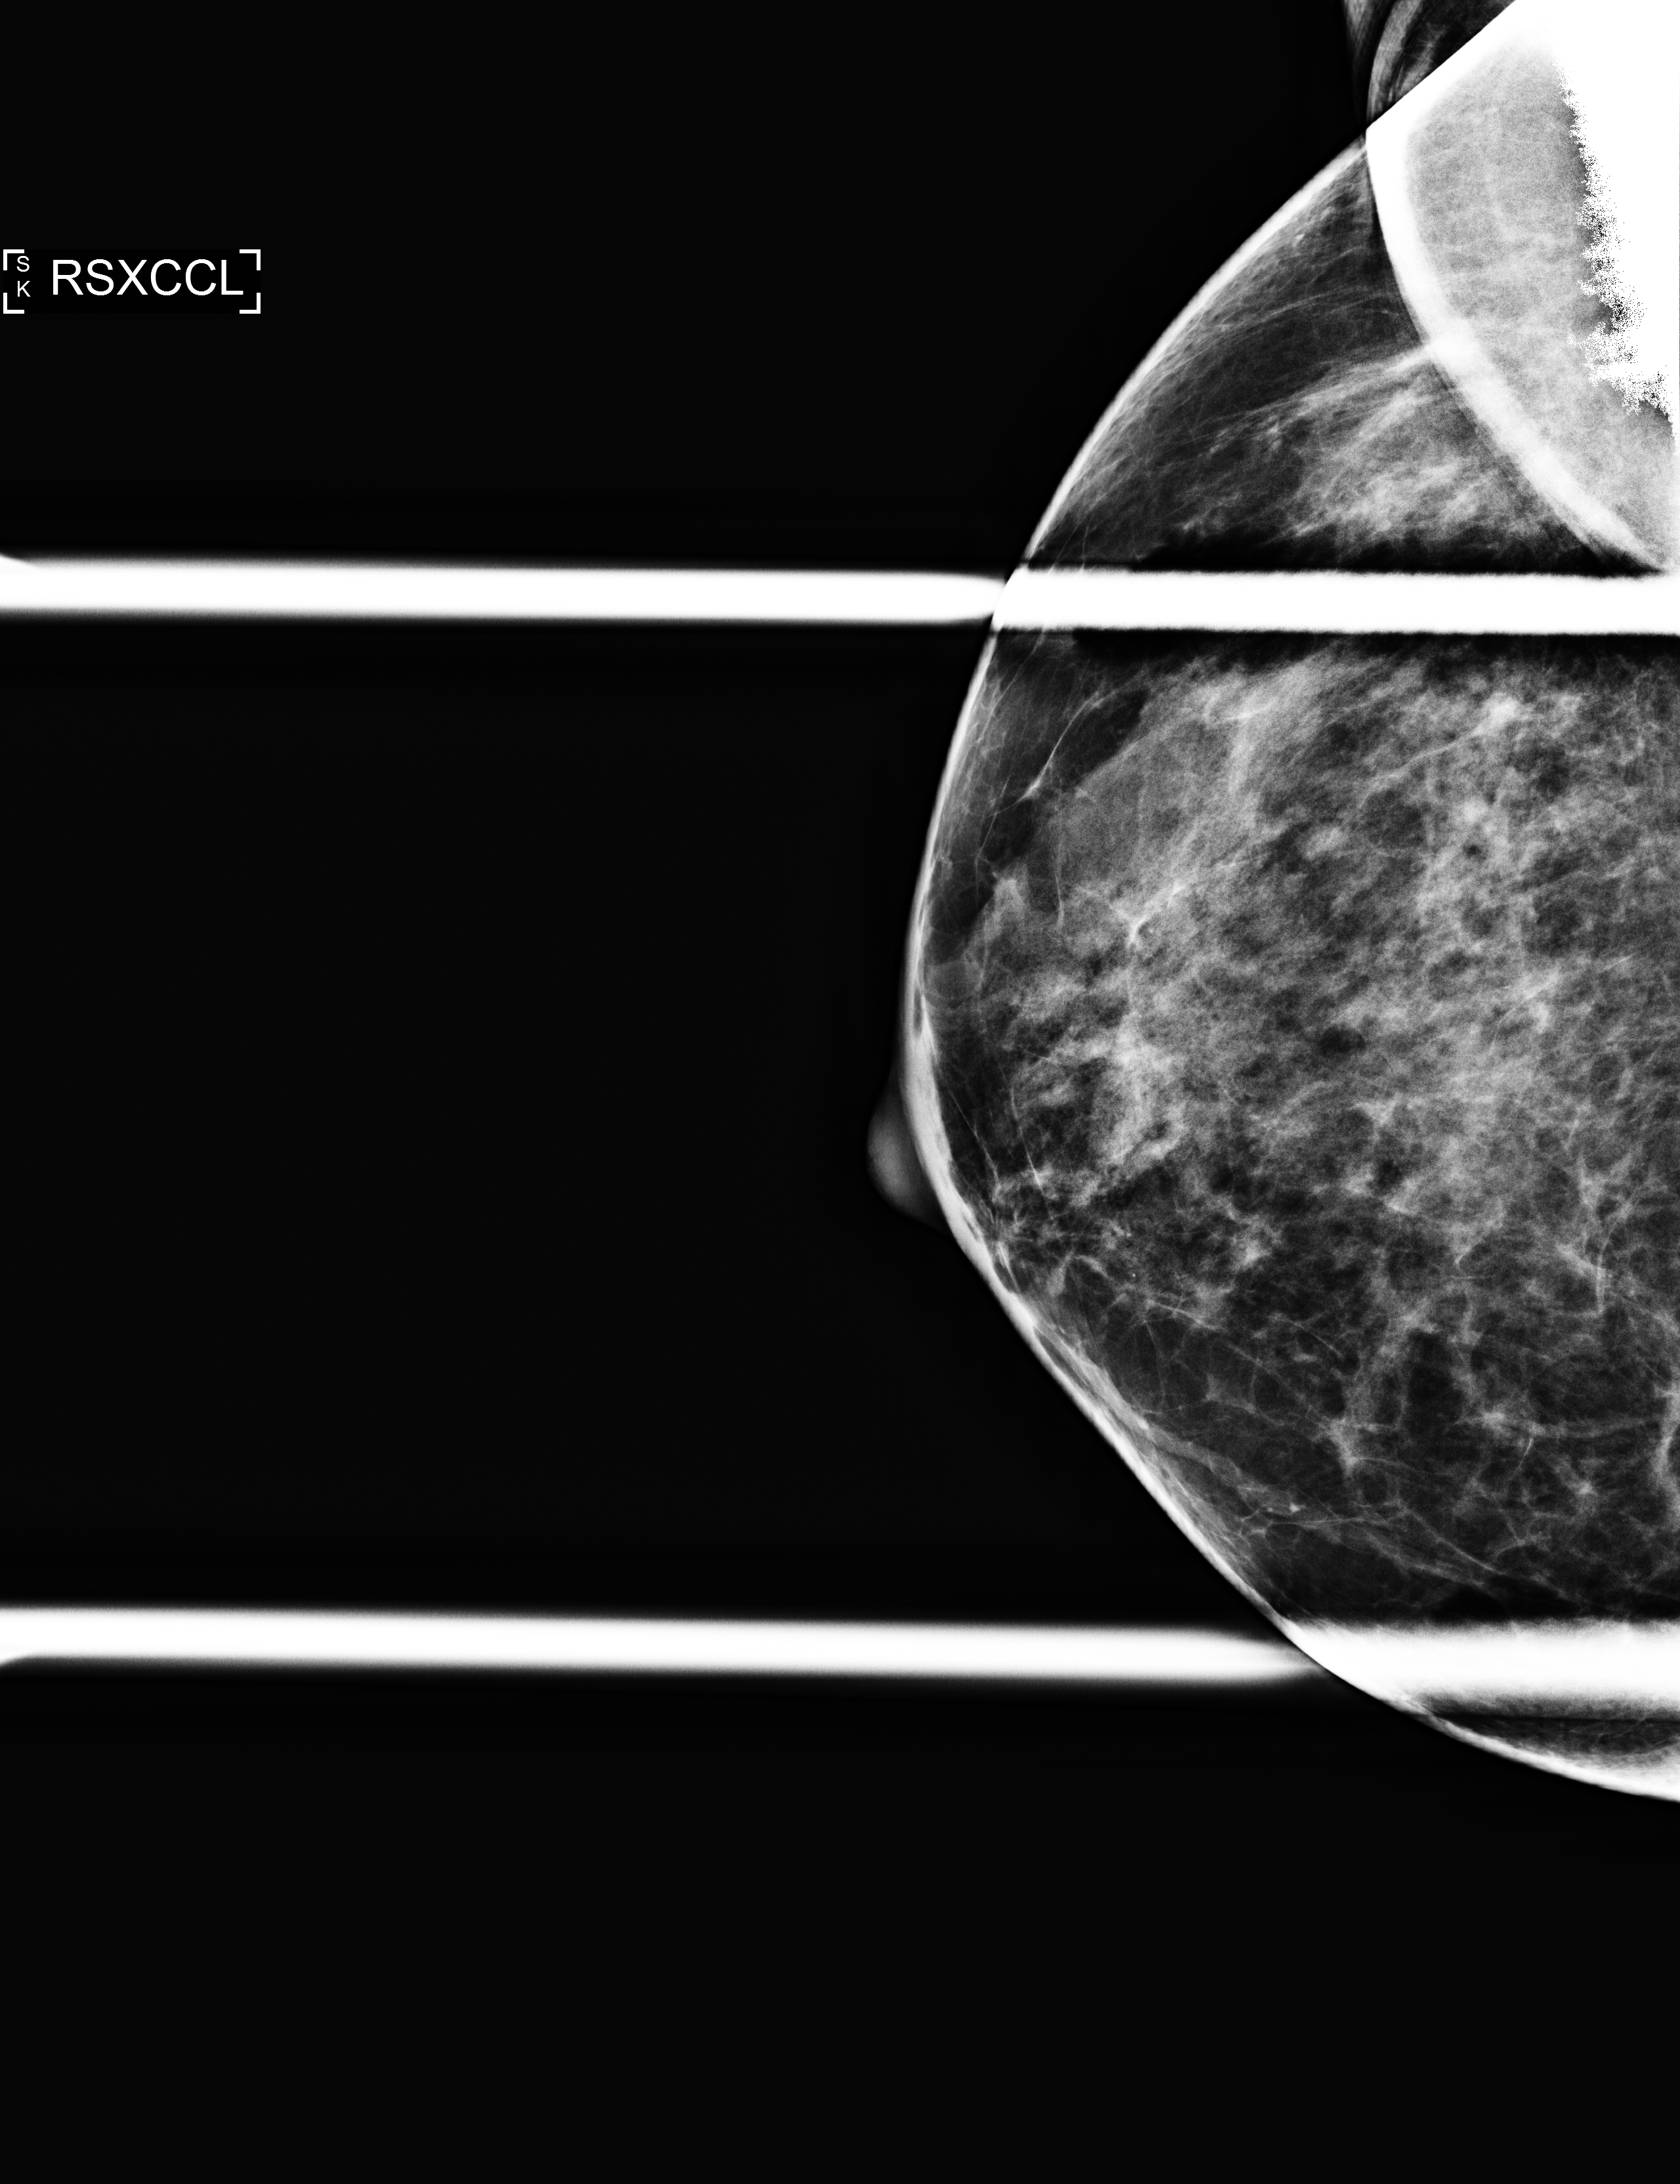
Digital mammogram (FFDM), right breast, laterally exaggerated craniocaudal (XCCL) view (spot compression), screening examination, compressed breast thickness 54 mm, system: Selenia Dimensions. Patient aged 59 years (female).
BI-RADS breast density category at the screening exam (both breasts, scale 1–4): 3. Final BI-RADS assessment for this screening round (tomosynthesis exam, both breasts): category 1. Recall: no recall after this screen.